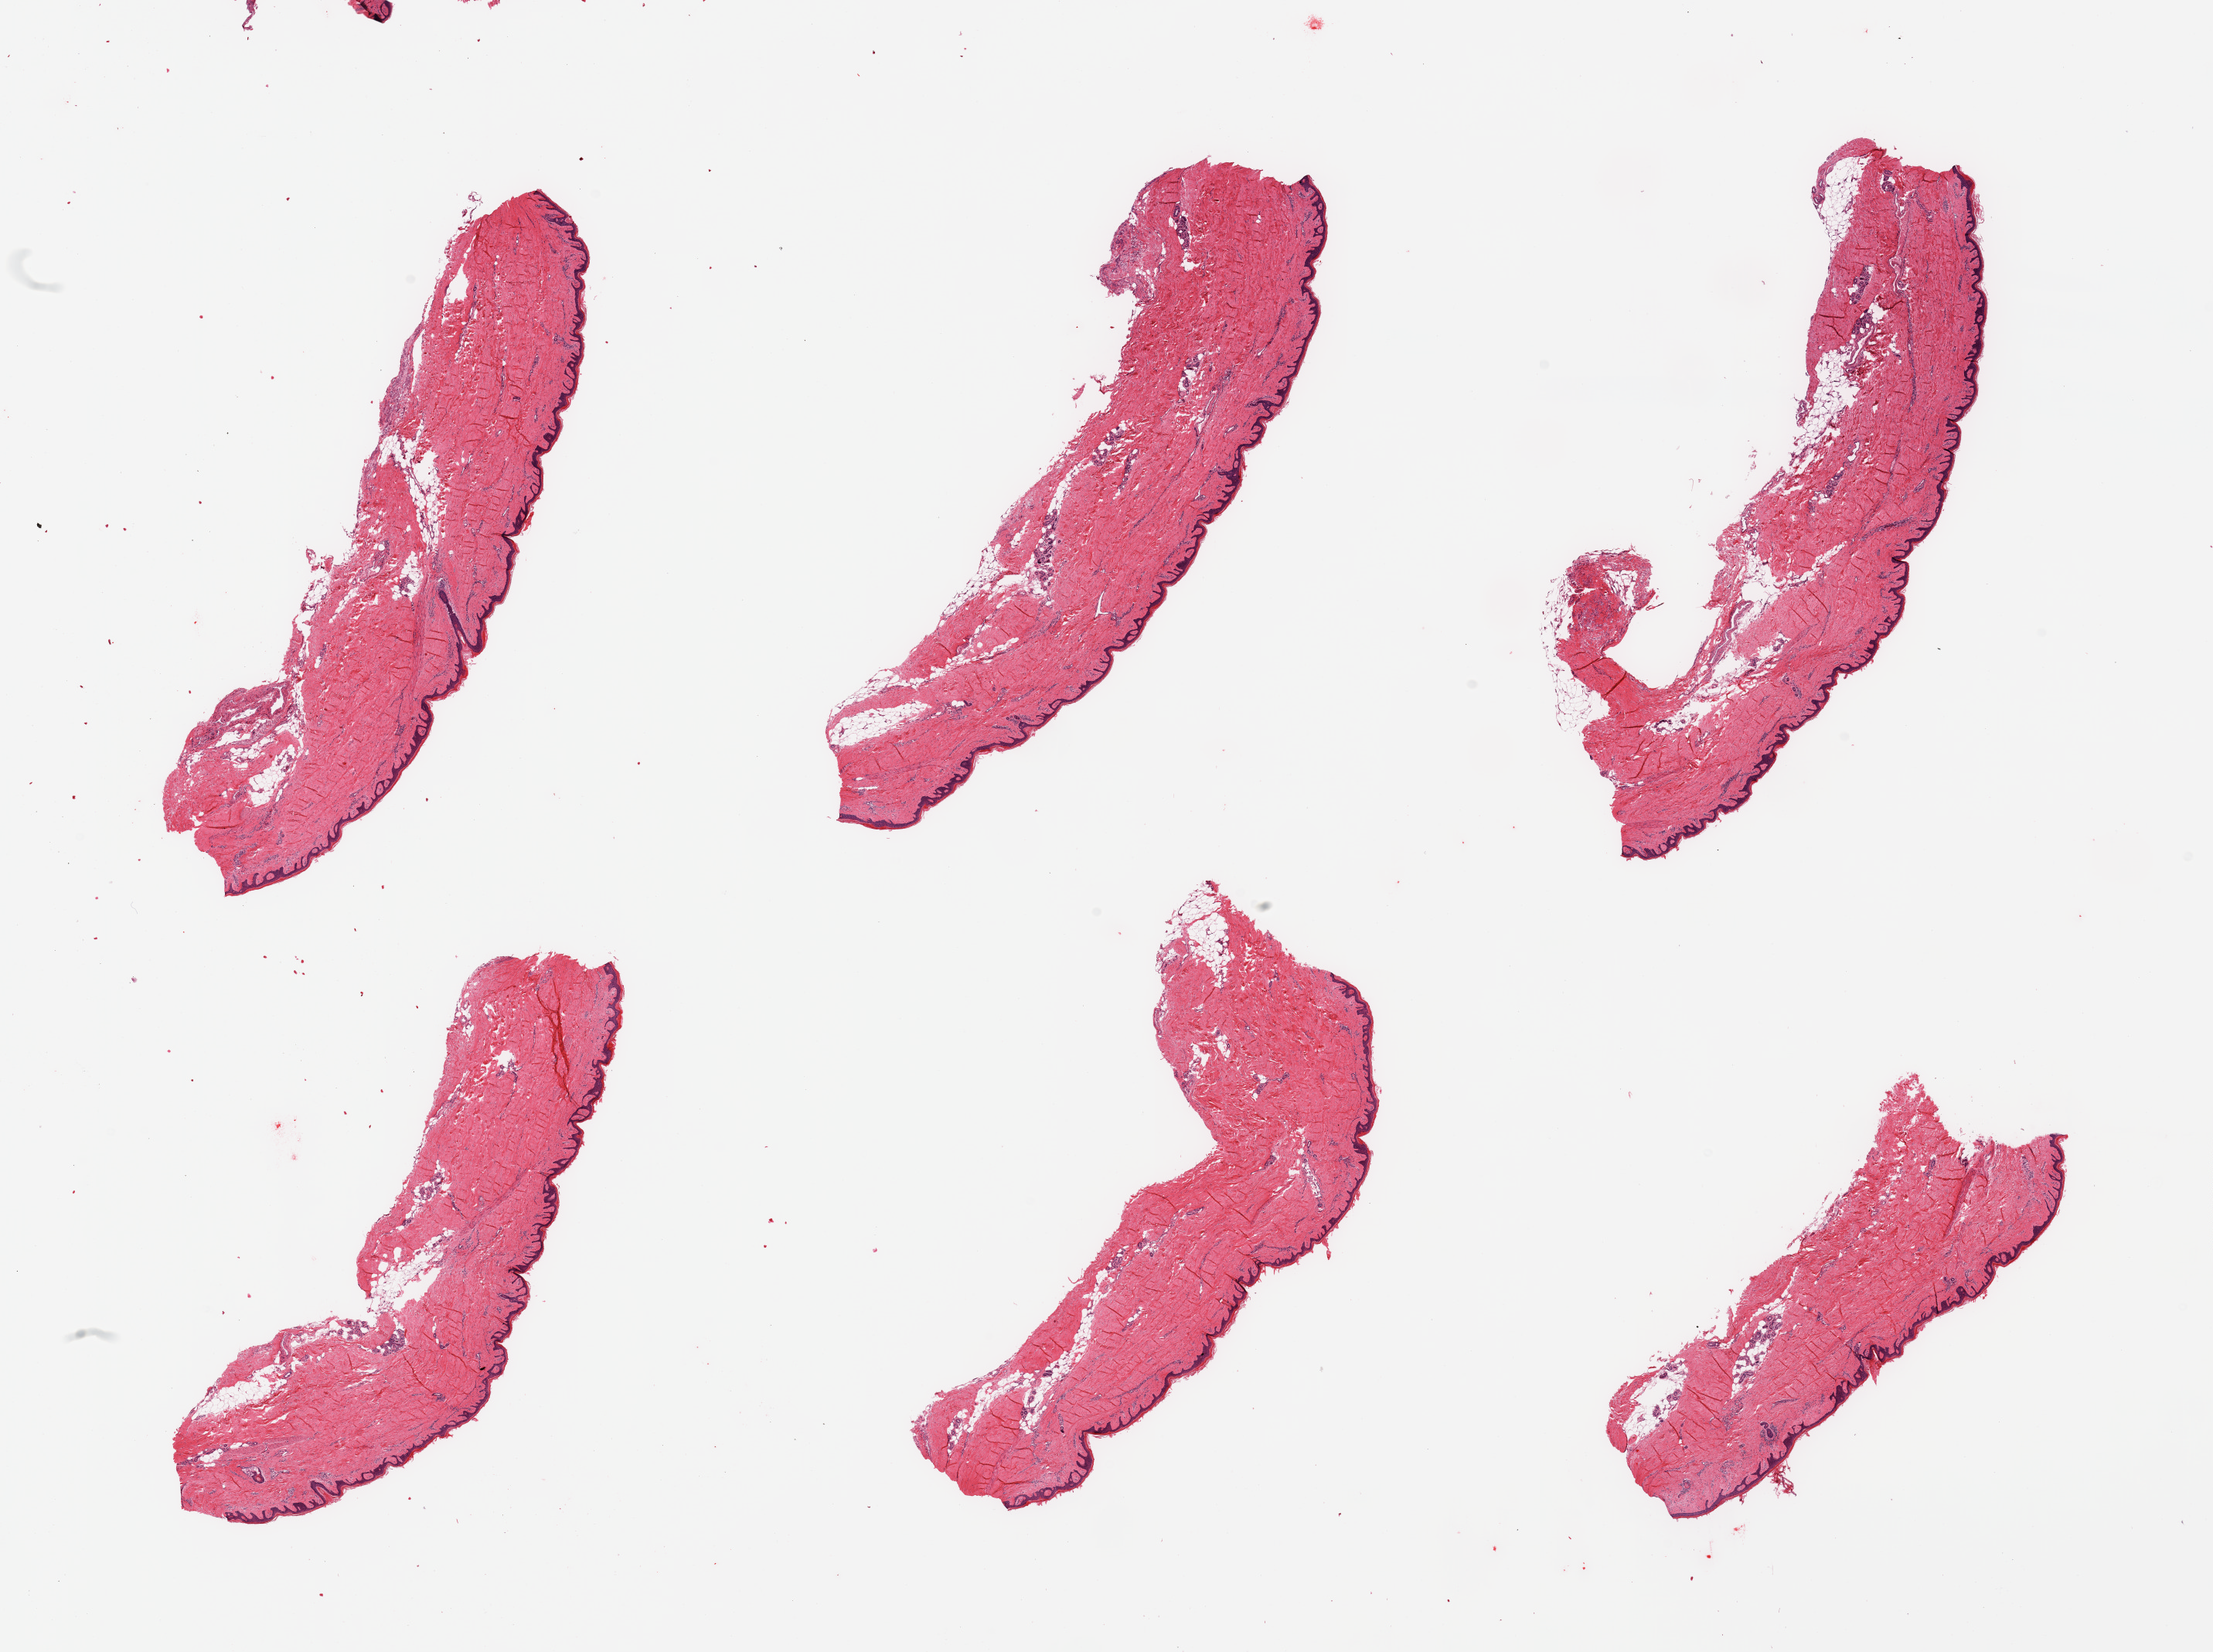
Whole-slide image, hematoxylin and eosin (H&E) stain — shown as a low-resolution overview of the whole scanned area (about 22.6 x 16.9 mm, acquisition: 20x scan); PAXgene-fixed, paraffin-embedded tissue; section of skin of lower leg (target tissue); tissue donor sample. Donor sex: female.
Review note (as recorded): 6 pieces; well trimmed; 5% dermal fat.